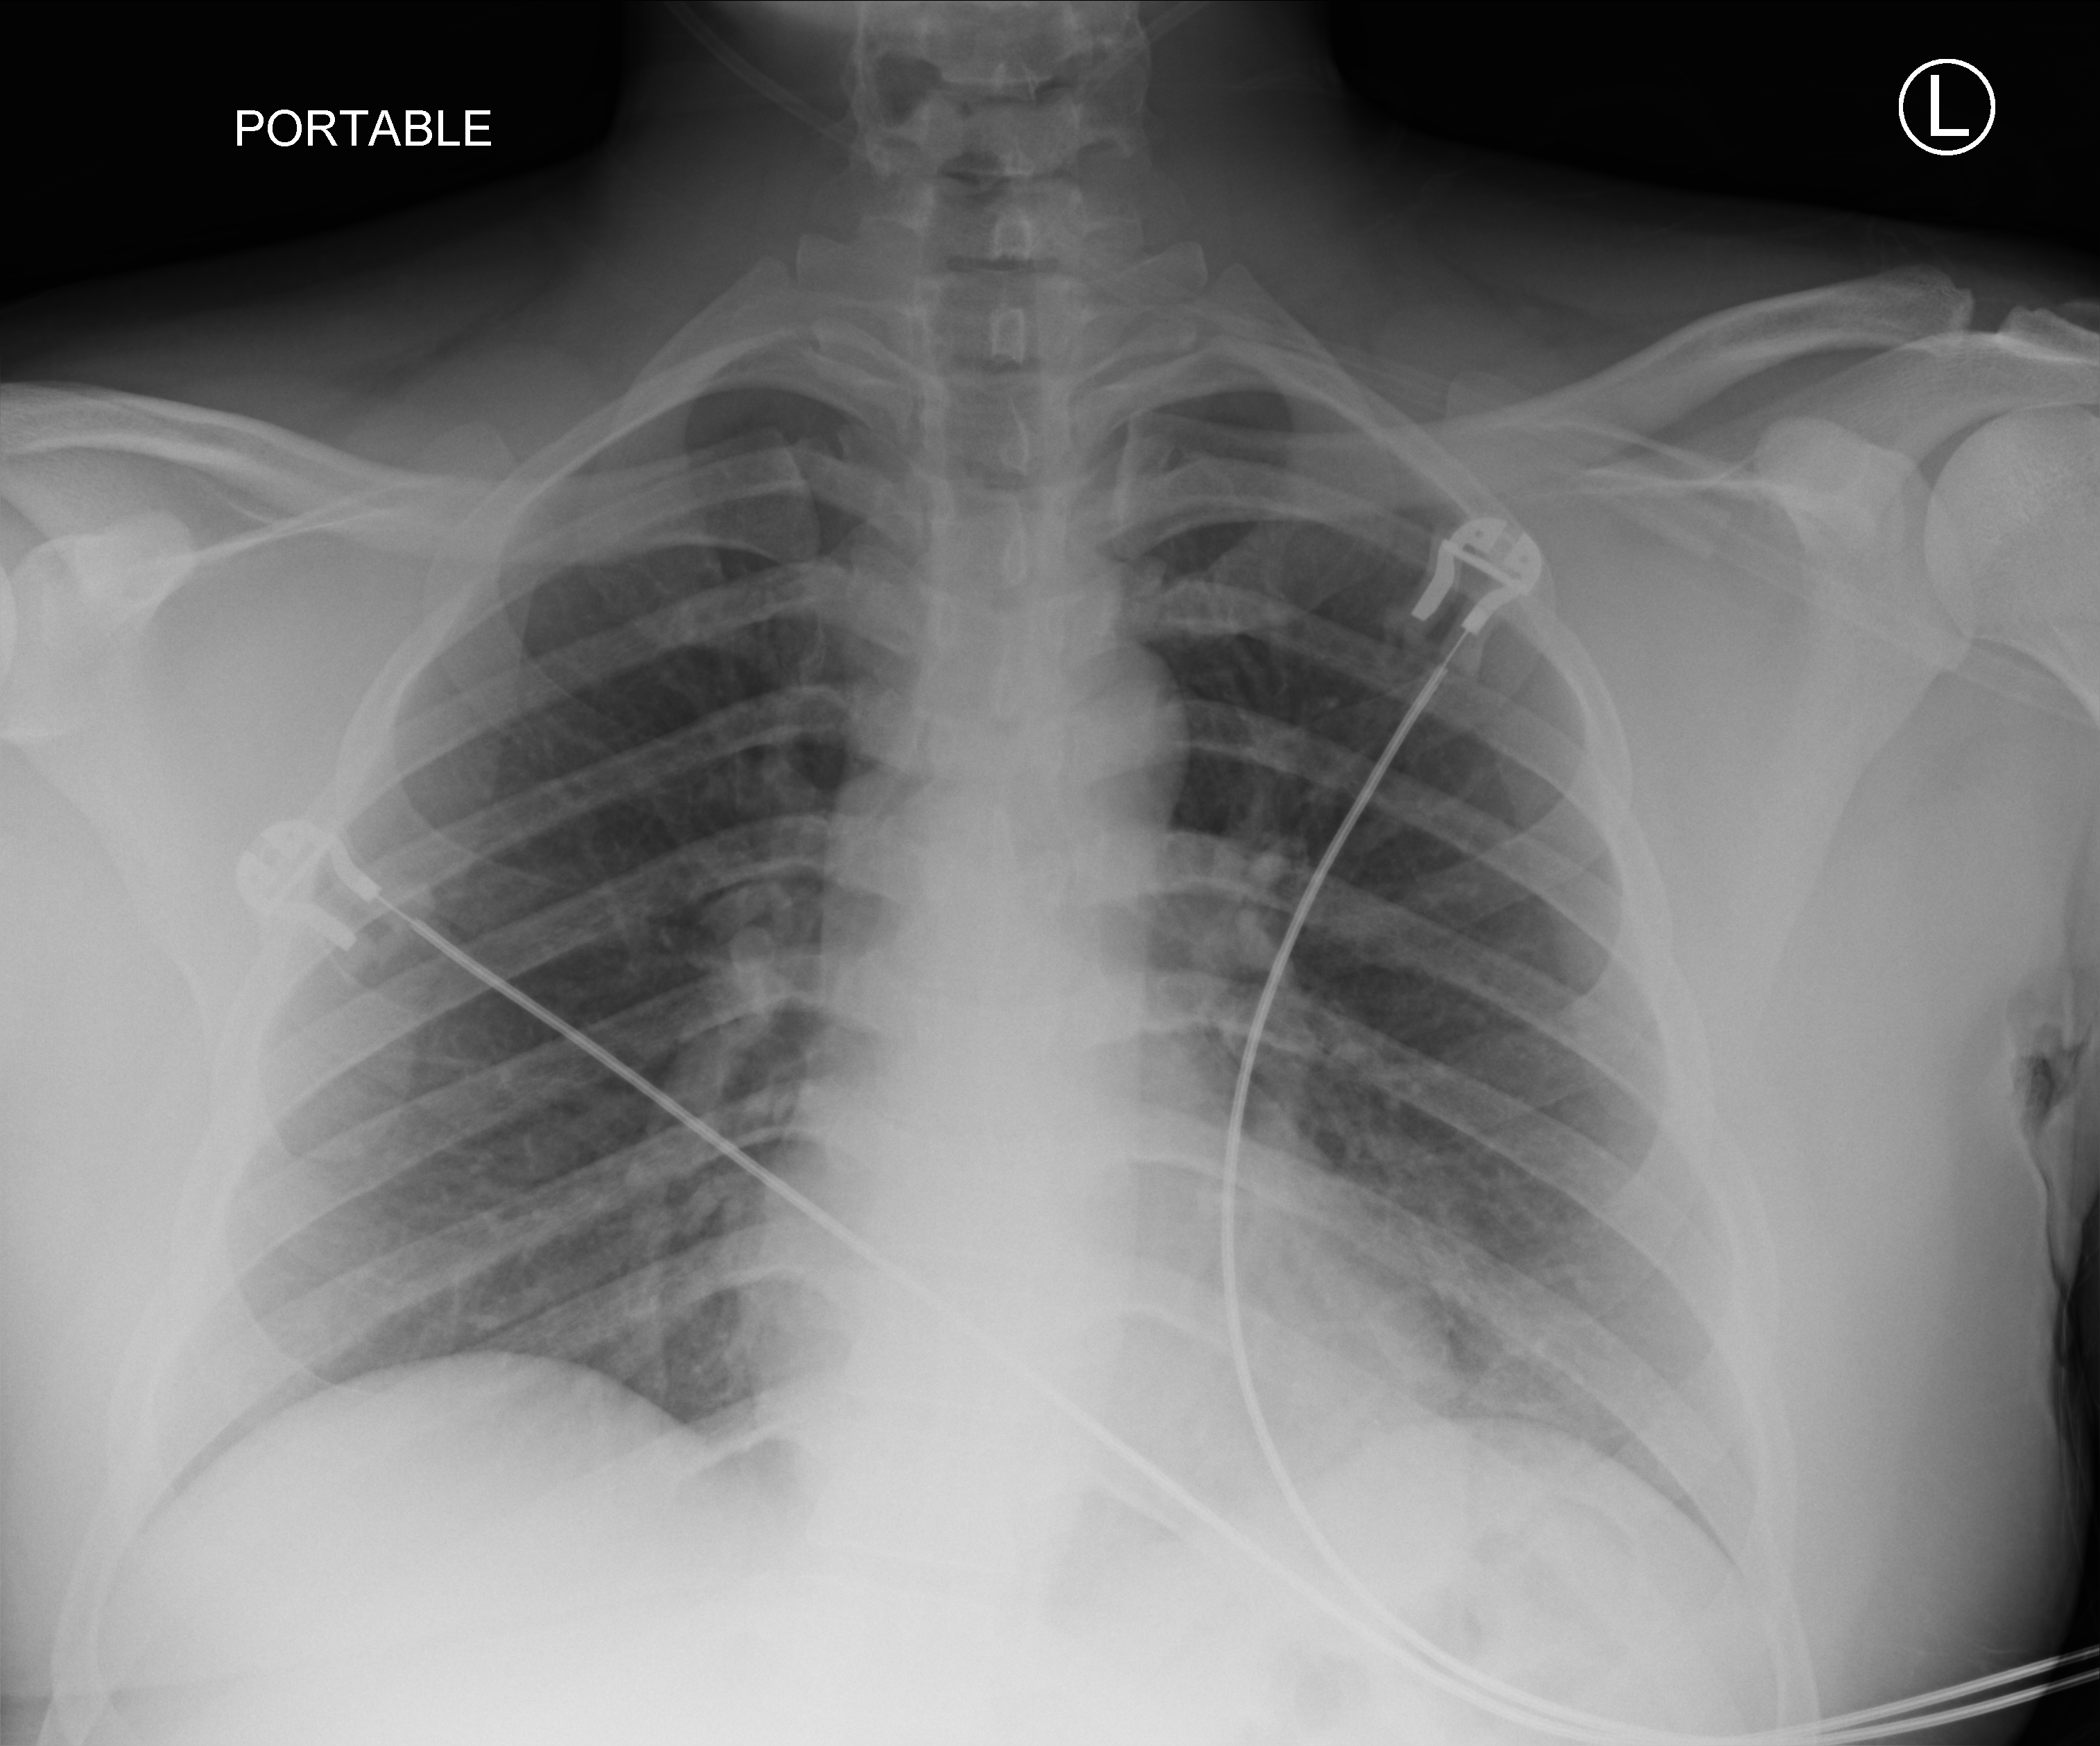
Portable chest radiograph, anteroposterior (AP) projection. Male patient hospitalised with COVID-19, age 18–59 years.
Hospital-stay facts (about this admission, not read from this image; timing relative to this image not recorded):
- mechanically ventilated during this hospital stay: no